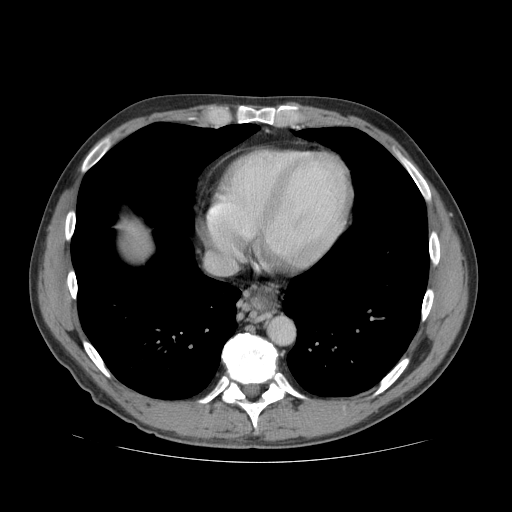
Contrast-enhanced abdominal CT (liver protocol), one axial slice; slice 74 of 81 in the series (ordered by position); reconstruction kernel STANDARD; 140 kVp; soft-tissue window (W 400 / L 40 HU); 2.5 mm slice thickness; 512 × 512 image matrix. From the clinical record (not read from this slice): diagnosis: hepatocellular carcinoma (patient treated with transarterial chemoembolisation; whether this scan precedes or follows treatment is not stated here); TNM stage (as recorded): Stage-IVB; Child-Pugh class: B; tumour differentiation: well differentiated; tumour nodularity: multinodular.
Outlined on this slice (semi-automatic segmentation, software-assisted and operator-edited):
- liver parenchyma outside the tumour (the mass and vessels are separate outlines, so this box may not span the whole liver): bounding box (x1, y1, x2, y2) in pixels: (124, 223, 150, 256)